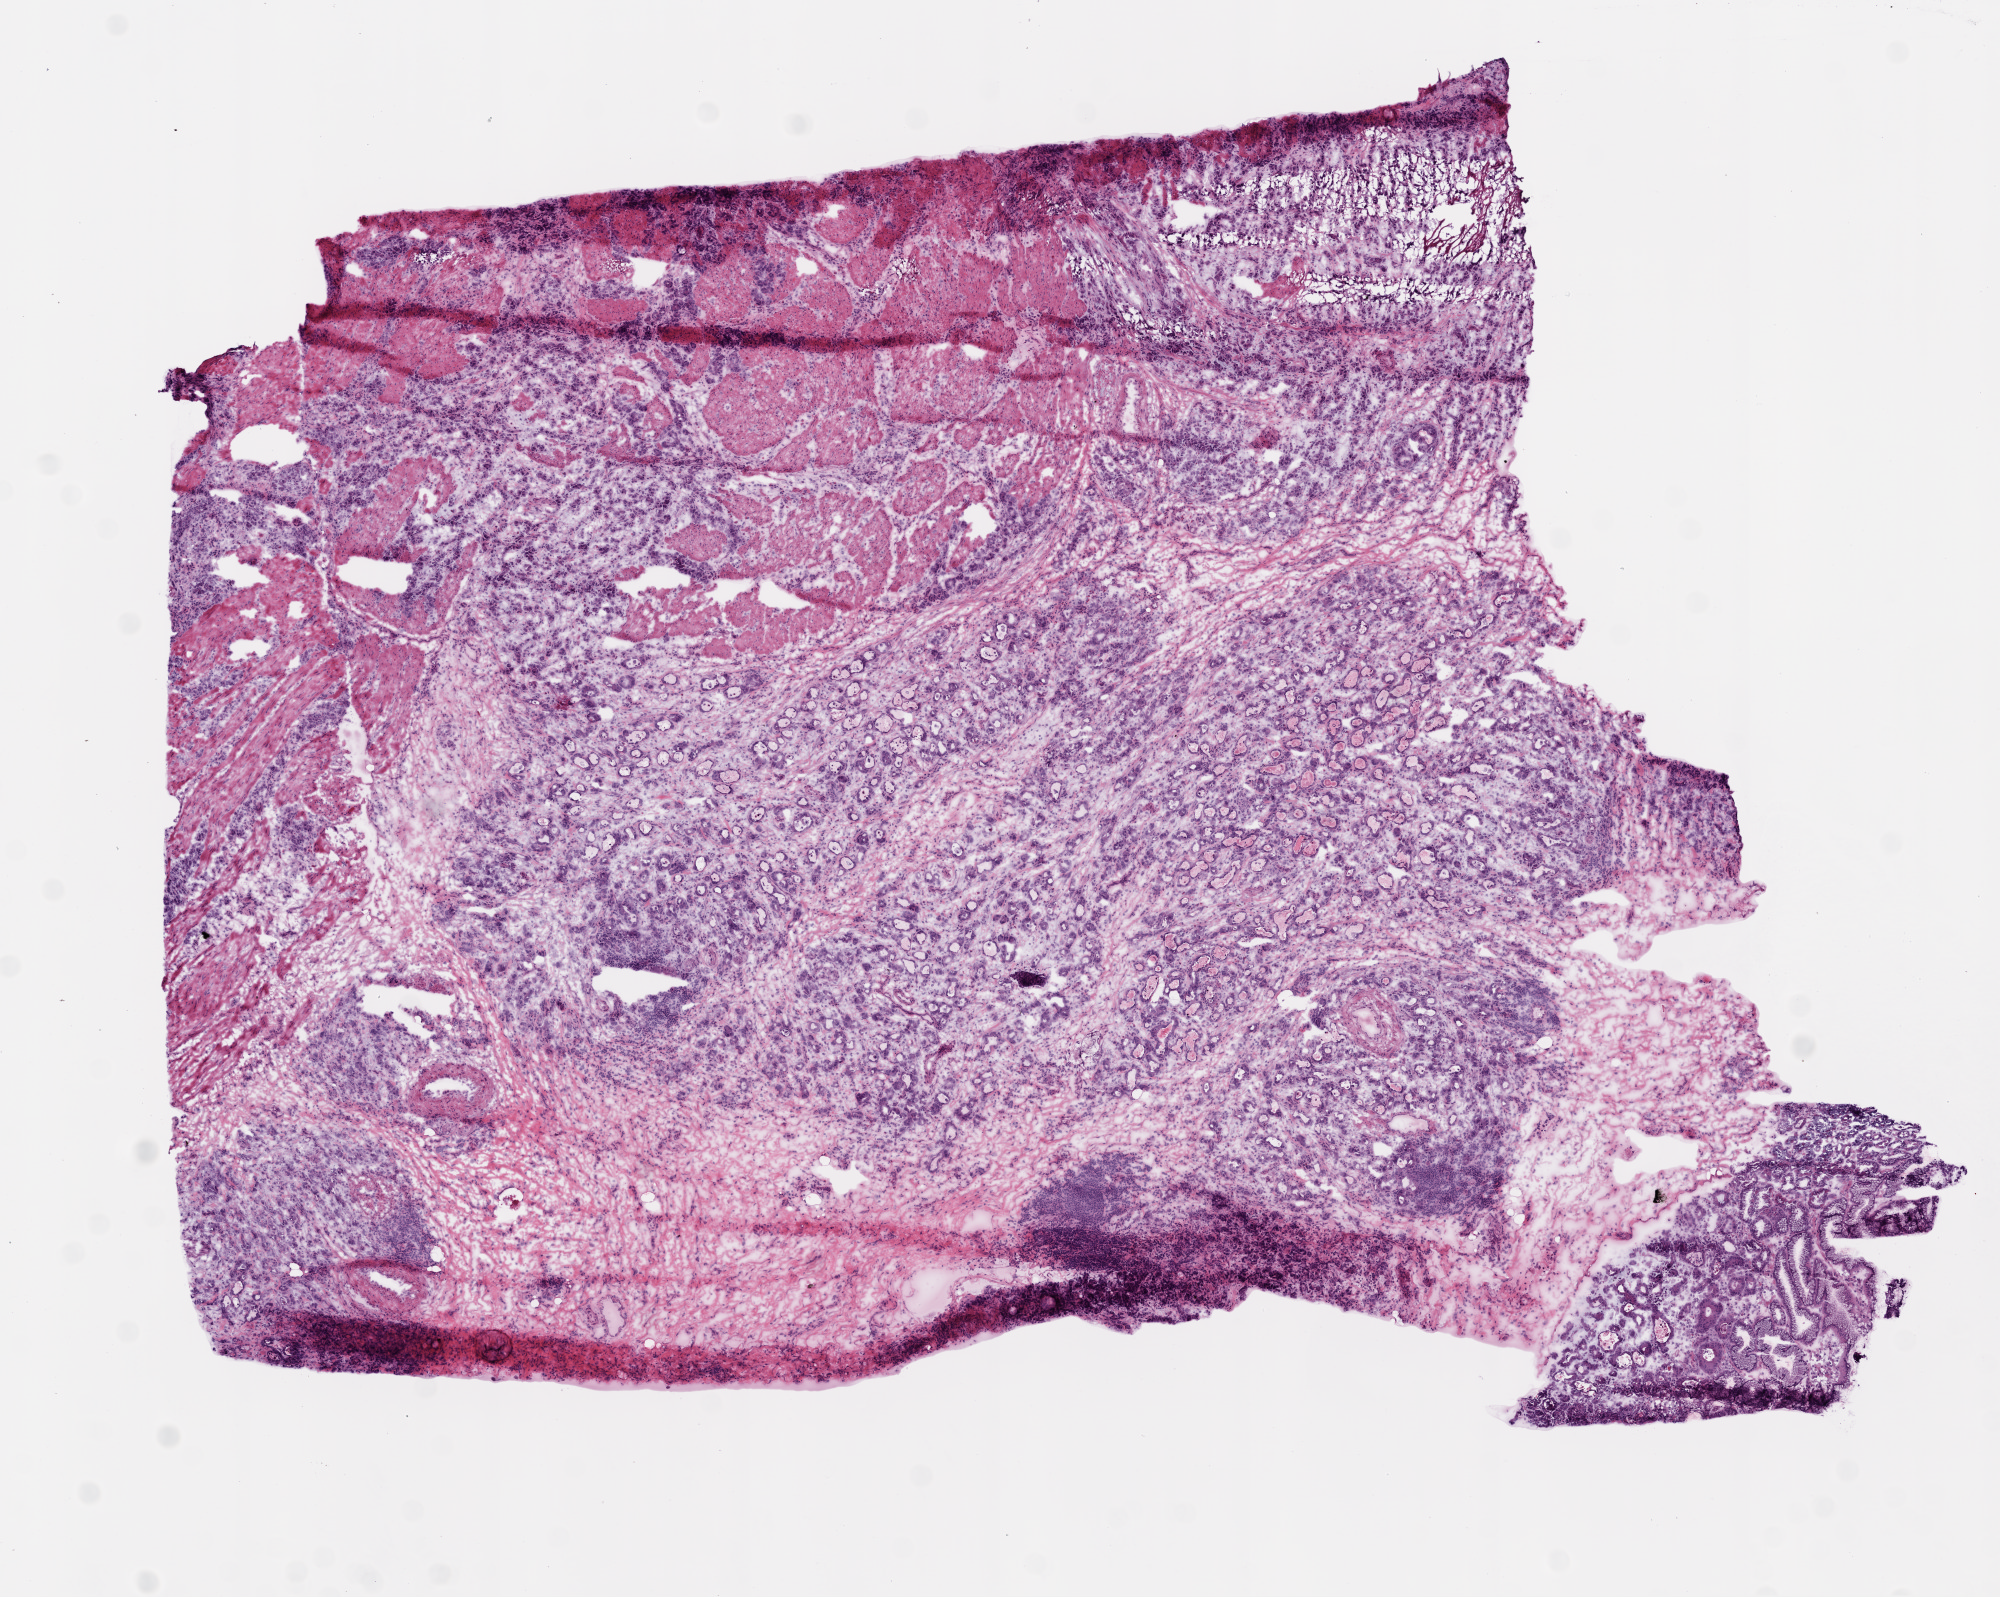
Whole-slide histology image, H&E-stained — low-resolution overview of the scanned area, about 8.0 x 6.4 mm (acquisition: 20x scan), frozen section from the top of the tissue portion, primary tumour sample from the stomach. Male patient; age at initial diagnosis 69 years. Histologic grade: G3 (poorly differentiated). Pathologist review of this section (percent, as recorded): tumour cells 70%, tumour nuclei 75%, normal cells 5%, stromal cells 20%, necrosis 5%.
AJCC pathologic stage: IIIC (7th edition). Pathologic diagnosis: Carcinoma, diffuse type (body of stomach). Lymph nodes positive (case pathology): 12 of 33 examined.